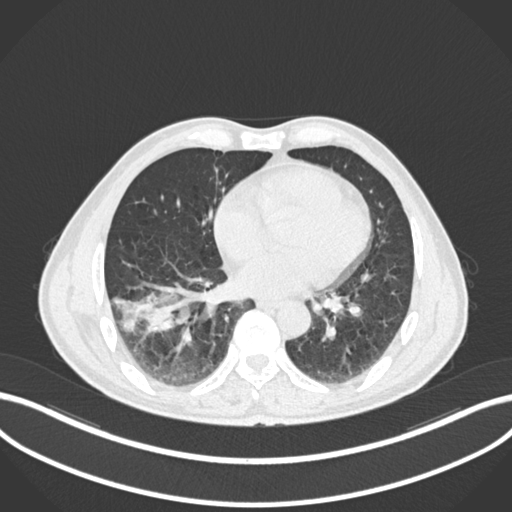
Chest CT, one axial slice. Slice 71 of 208 in the series (ordered by position). Reconstruction kernel B30f. Lung window (W 1500 / L -600 HU). 512 × 512 image matrix, field of view 400 × 400 mm. Male patient, age 58 years. From the clinical record (not read from this slice): clinical TNM (as recorded): T3 N0 M0; histopathological grade: G2.
Outlined on this slice (bounding box drawn by a radiologist):
- lung tumour (recorded histology: squamous cell carcinoma): box from (x=115, y=276) to (x=194, y=337) px